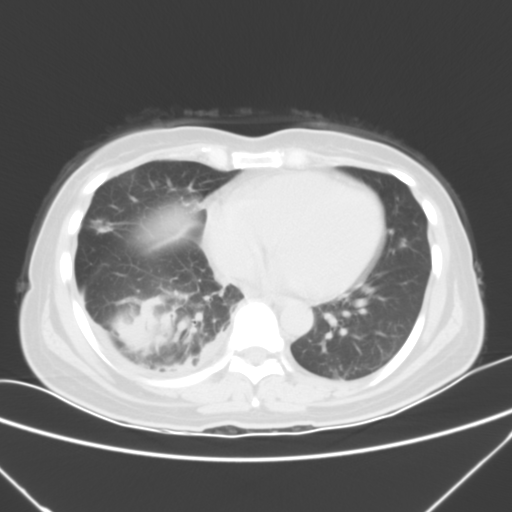
Chest CT, one axial slice. Position 17 of 53 along the scan axis. 120 kVp. Lung window (W 1500 / L -600 HU). 5 mm slice thickness. 512 × 512 image matrix, field of view 337 × 337 mm. Patient: female, 42 years. Case-level facts recorded for this patient, not image findings: clinical TNM (as recorded): T3 N0 M1c.
Structures marked on this image (rectangle marked by the reading radiologist):
- lung tumour (recorded histology: adenocarcinoma): bounding box (x1, y1, x2, y2) in pixels: (104, 298, 176, 368)